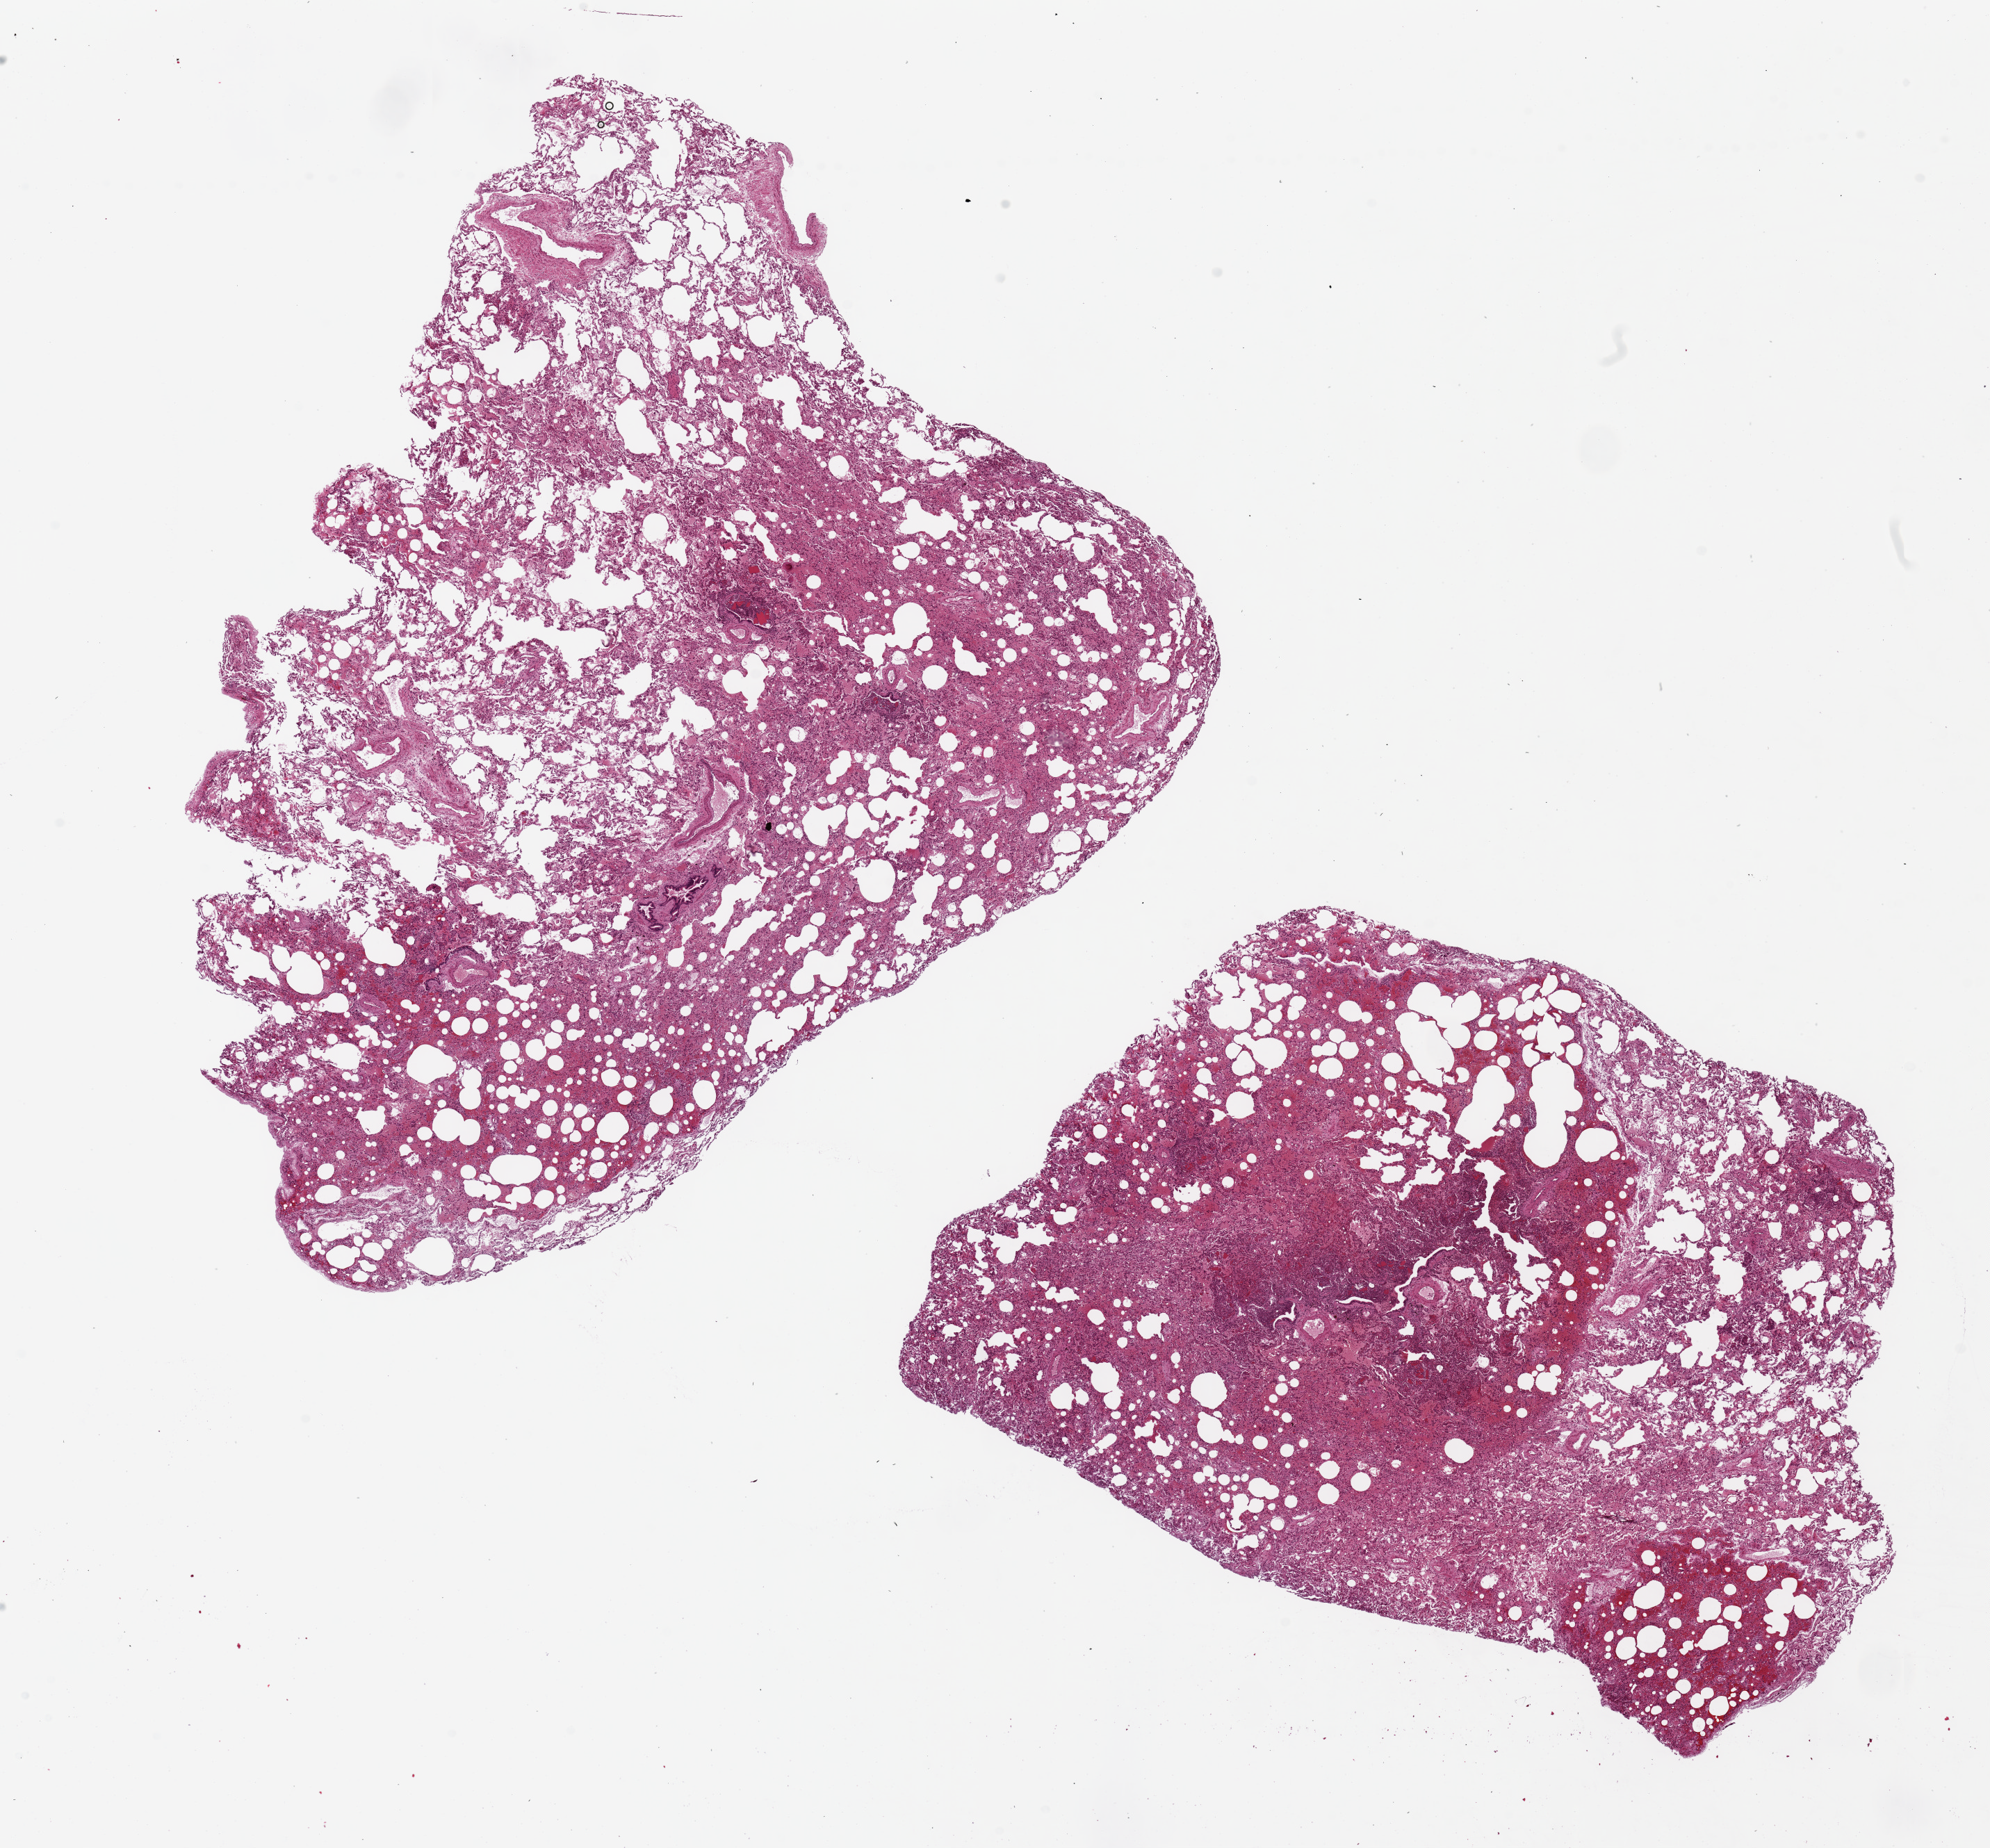
Digitized haematoxylin and eosin-stained section, brightfield — shown as a low-resolution overview of the whole scanned area (about 22.6 x 21.0 mm); PAXgene-fixed, paraffin-embedded tissue; target tissue: lung; donor tissue sample. Donor sex: male.
* reviewer comment on this tissue sample: 2 pieces ~8x7mm. Patchy consolidation with acute aspiration pneumonia, foreign material in bronchi and parenchma, focal foreign body giant cell reaction